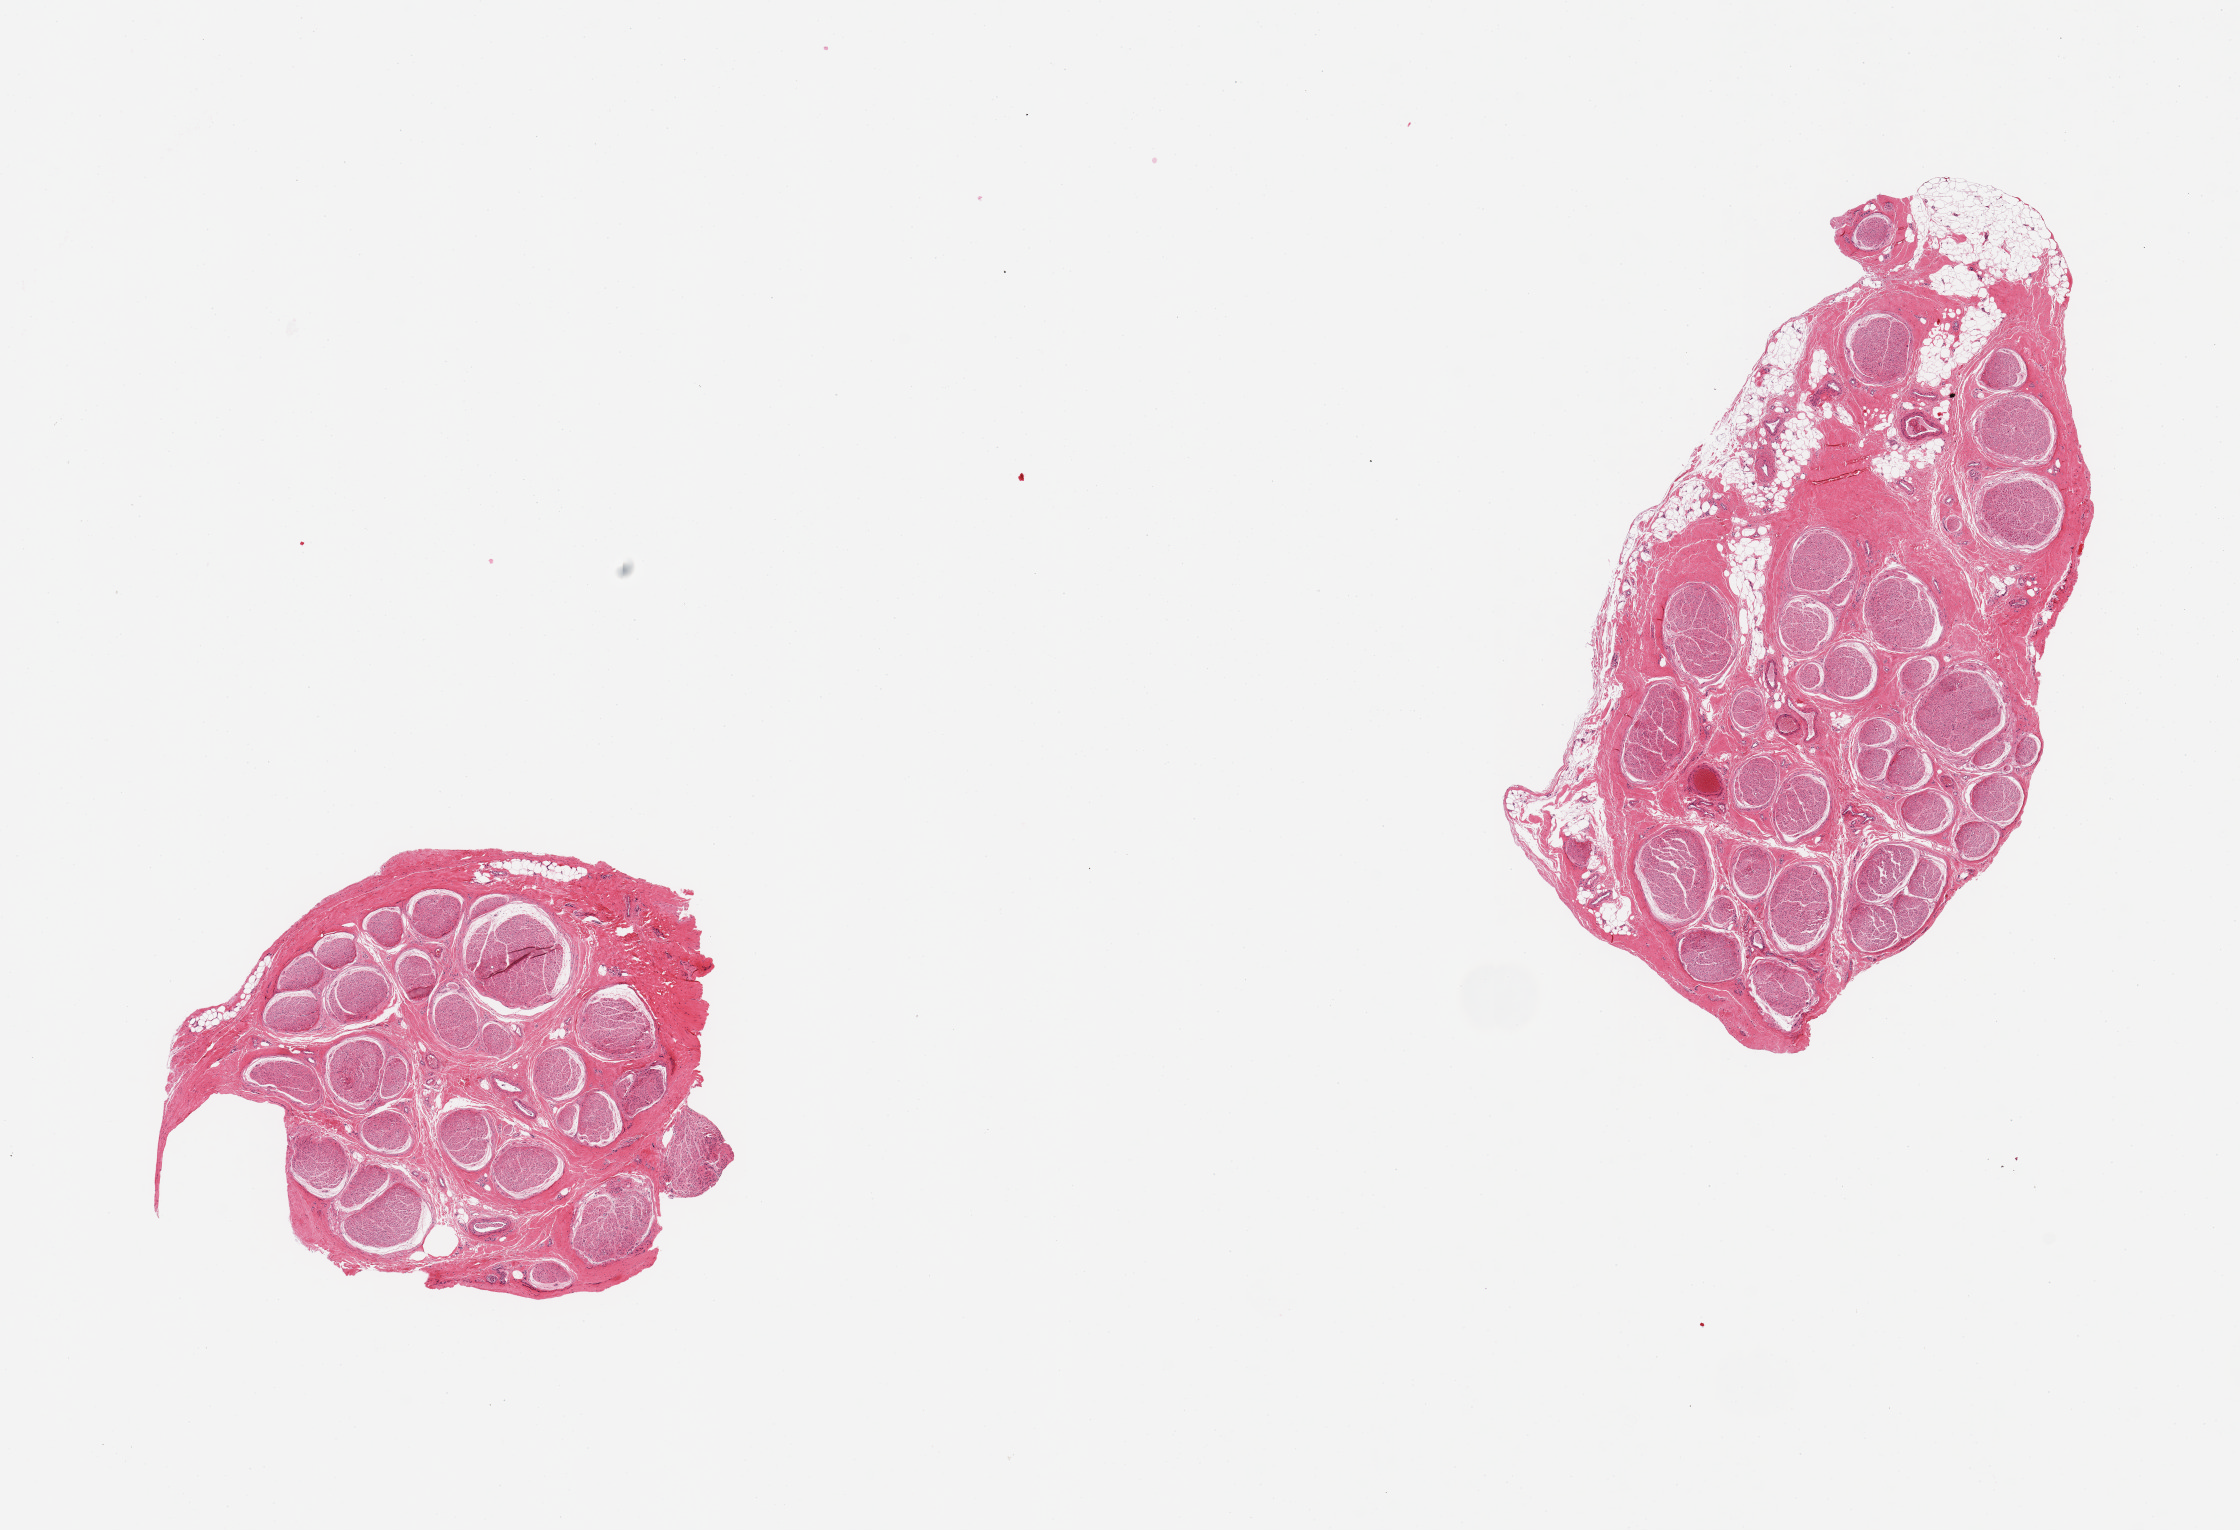
Whole-slide image, haematoxylin and eosin stain, shown as a low-resolution overview of the whole scanned area (about 17.7 x 12.1 mm, slide scanned at 20x). PAXgene-fixed, paraffin-embedded tissue. Target tissue: tibial nerve. Donor tissue sample. Donor: male.
Pathologist's review note for this sample: 2 pieces, trace adherent fat.